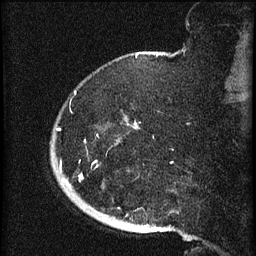
Breast MRI (dynamic contrast-enhanced), one sagittal slice; position 12 of 60 along the scan axis; dynamic contrast-enhanced series, image 2 of 3 at this slice position (ordered by acquisition); 1.5 T; TE 4.2 ms, TR 8.2 ms; 256 × 256 image matrix, field of view 180 × 180 mm. Female patient, age 71 years.
Outlined on this slice (semi-automatically segmented with operator editing):
- analysis volume of interest (the breast-tissue region the enhancement analysis was run in; not a lesion): bounding box (x1, y1, x2, y2) in pixels: (51, 85, 139, 196)
- tumour enhancement mask (voxels above the 70 % enhancement threshold inside the analysis volume of interest): (57, 128, 83, 178)